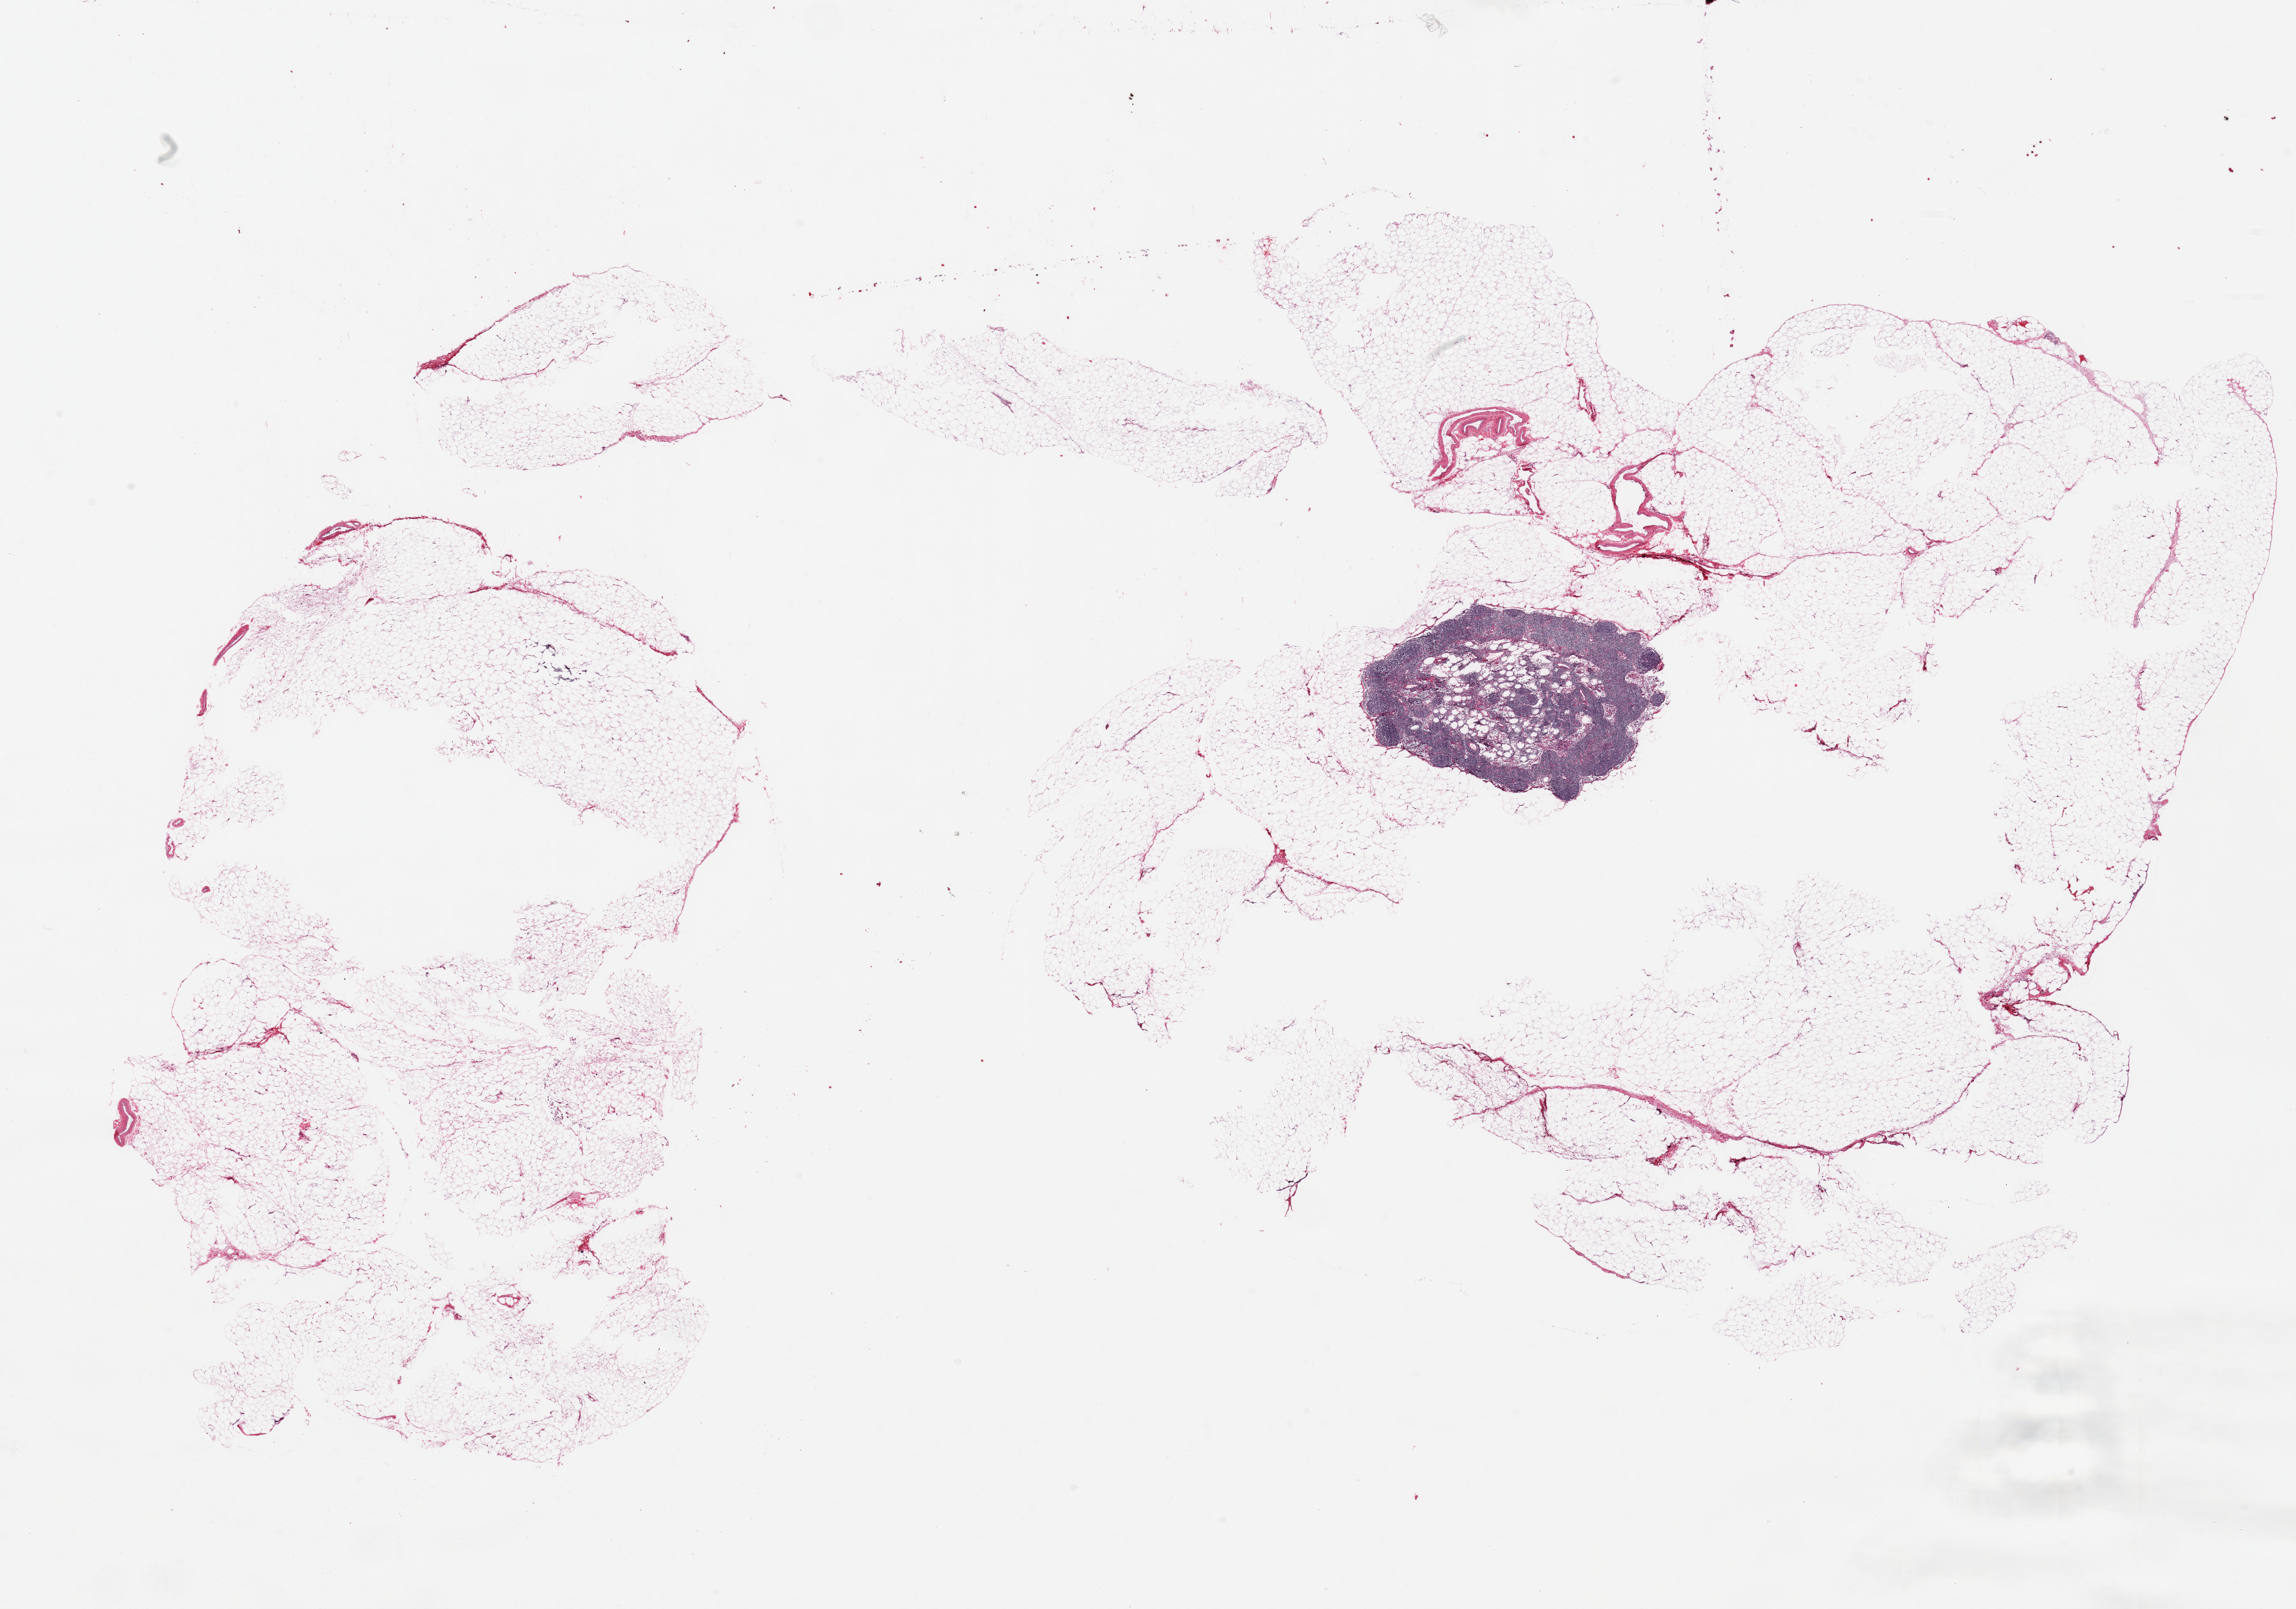
Whole-slide image, hematoxylin and eosin (H&E) stain, whole scanned area (about 28.5 x 20.0 mm, acquisition: 20x scan) shown as a low-resolution overview. PAXgene-fixed paraffin-embedded (PFPE) section. Sampled site (target tissue): omentum. Tissue donor sample. Donor sex: male.
• reviewer comment on this tissue sample: 2 pieces; some central defects; incidental 3.8mm lymph node